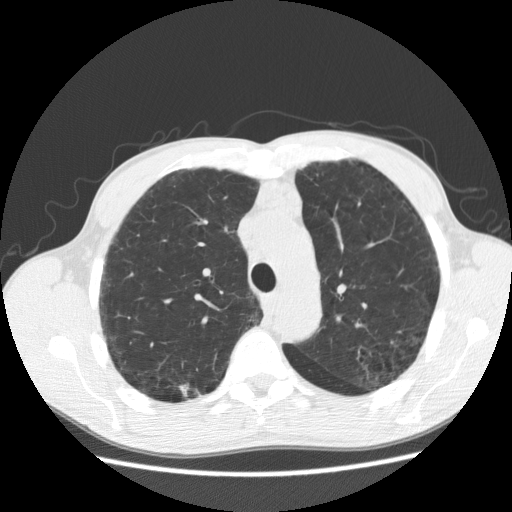
Low-dose screening chest CT, one axial slice; position 140 of 195 along the scan axis; reconstruction kernel STANDARD; 120 kVp; lung window (W 1500 / L -600 HU); 2.5 mm slice thickness; 512 × 512 image matrix, field of view 355 × 355 mm.
Outlined on this slice (outlined manually by an expert reader):
- lesion 1 (tumor, upper lobe of right lung): bounding box (x1, y1, x2, y2) in pixels: (180, 384, 190, 397)